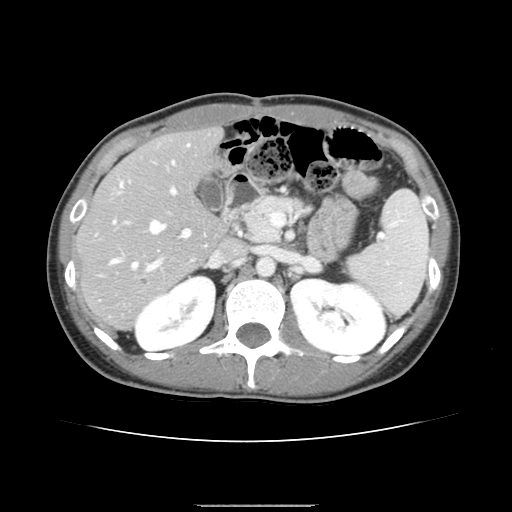
Contrast-enhanced abdominal CT, one axial slice. Position 85 of 150 along the scan axis. Intravenous contrast given. Soft-tissue window (W 400 / L 40 HU). 512 × 512 image matrix, field of view 324 × 324 mm. Female patient, age 32 years. From the clinical record (not read from this slice): diagnosis: colorectal cancer liver metastases, imaged before liver resection; multiple liver metastases: yes; largest metastasis: 0.7 cm; disease in both lobes: no.
Structures marked on this image (outlined manually by an expert reader):
- hepatic veins: box from (x=112, y=144) to (x=189, y=267) px
- liver: (x=78, y=129)–(x=226, y=329)
- planned liver remnant (the part of the liver to remain after resection): (x=78, y=129)–(x=226, y=276)
- portal vein (with intrahepatic branches): (x=109, y=186)–(x=190, y=271)
- liver metastasis: (x=141, y=281)–(x=146, y=285)